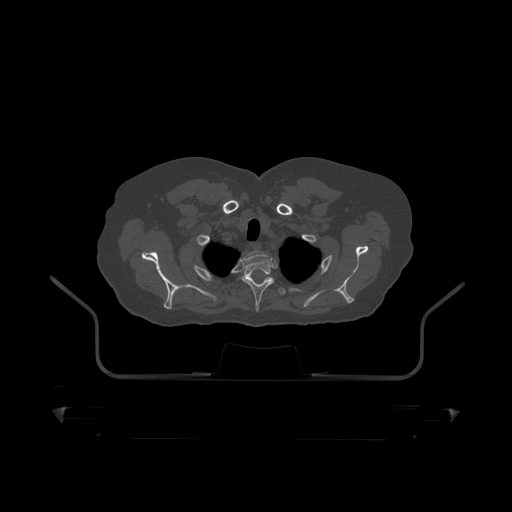
CT including the spine, one axial slice; position 374 of 390 along the scan axis; reconstruction kernel STANDARD; 120 kVp; bone window (W 1800 / L 400 HU); 1.25 mm slice thickness; 512 × 512 image matrix. Patient: male, 60 years. From the clinical record (not read from this slice): primary cancer: prostate.
Outlined on this slice (semi-automatic segmentation, software-assisted and operator-edited):
- T1 vertebra: box from (x=240, y=252) to (x=263, y=268) px
- T2 vertebra: (x=242, y=259)–(x=275, y=310)
- T3 vertebra: (x=247, y=276)–(x=286, y=296)